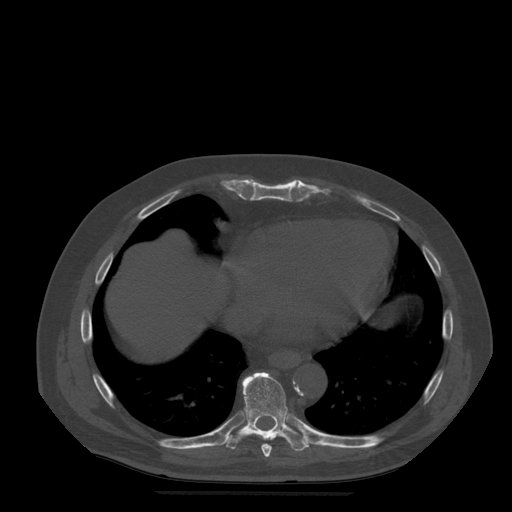
CT including the spine, one axial slice. Position 296 of 522 along the scan axis. Bone window (W 1800 / L 400 HU). 512 × 512 image matrix, field of view 420 × 420 mm. Patient age 72 years. Case-level facts recorded for this patient, not image findings: primary cancer: prostate.
Structures marked on this image (semi-automatically segmented with operator editing):
- T8 vertebra: bounding box [x1, y1, x2, y2] px = [262, 444, 272, 457]
- T9 vertebra: [226, 372, 309, 451]